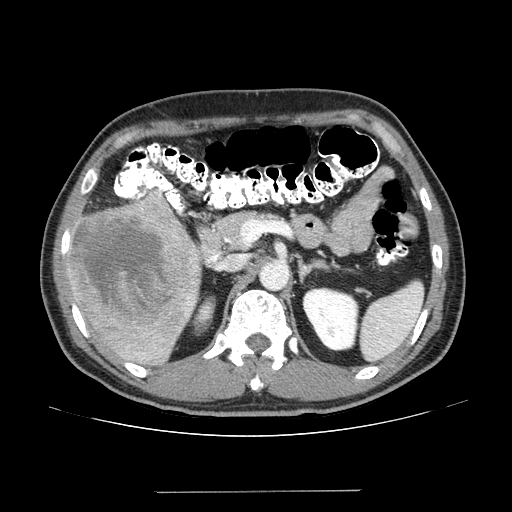
Contrast-enhanced abdominal CT (liver protocol), one axial slice; one of 2 acquisitions stored at this slice position; soft-tissue window (W 400 / L 40 HU); 512 × 512 image matrix, field of view 380 × 380 mm. From the clinical record (not read from this slice): diagnosis: hepatocellular carcinoma (patient treated with transarterial chemoembolisation; whether this scan precedes or follows treatment is not stated here); TNM stage (as recorded): Stage-I; Child-Pugh class: A; tumour differentiation: poorly differentiated; tumour nodularity: uninodular.
Structures marked on this image (semi-automatic segmentation, software-assisted and operator-edited):
- liver parenchyma outside the tumour (the mass and vessels are separate outlines, so this box may not span the whole liver): bounding box <66,192,200,364> (left, top, right, bottom; pixels)
- mass: <71,193,198,327>